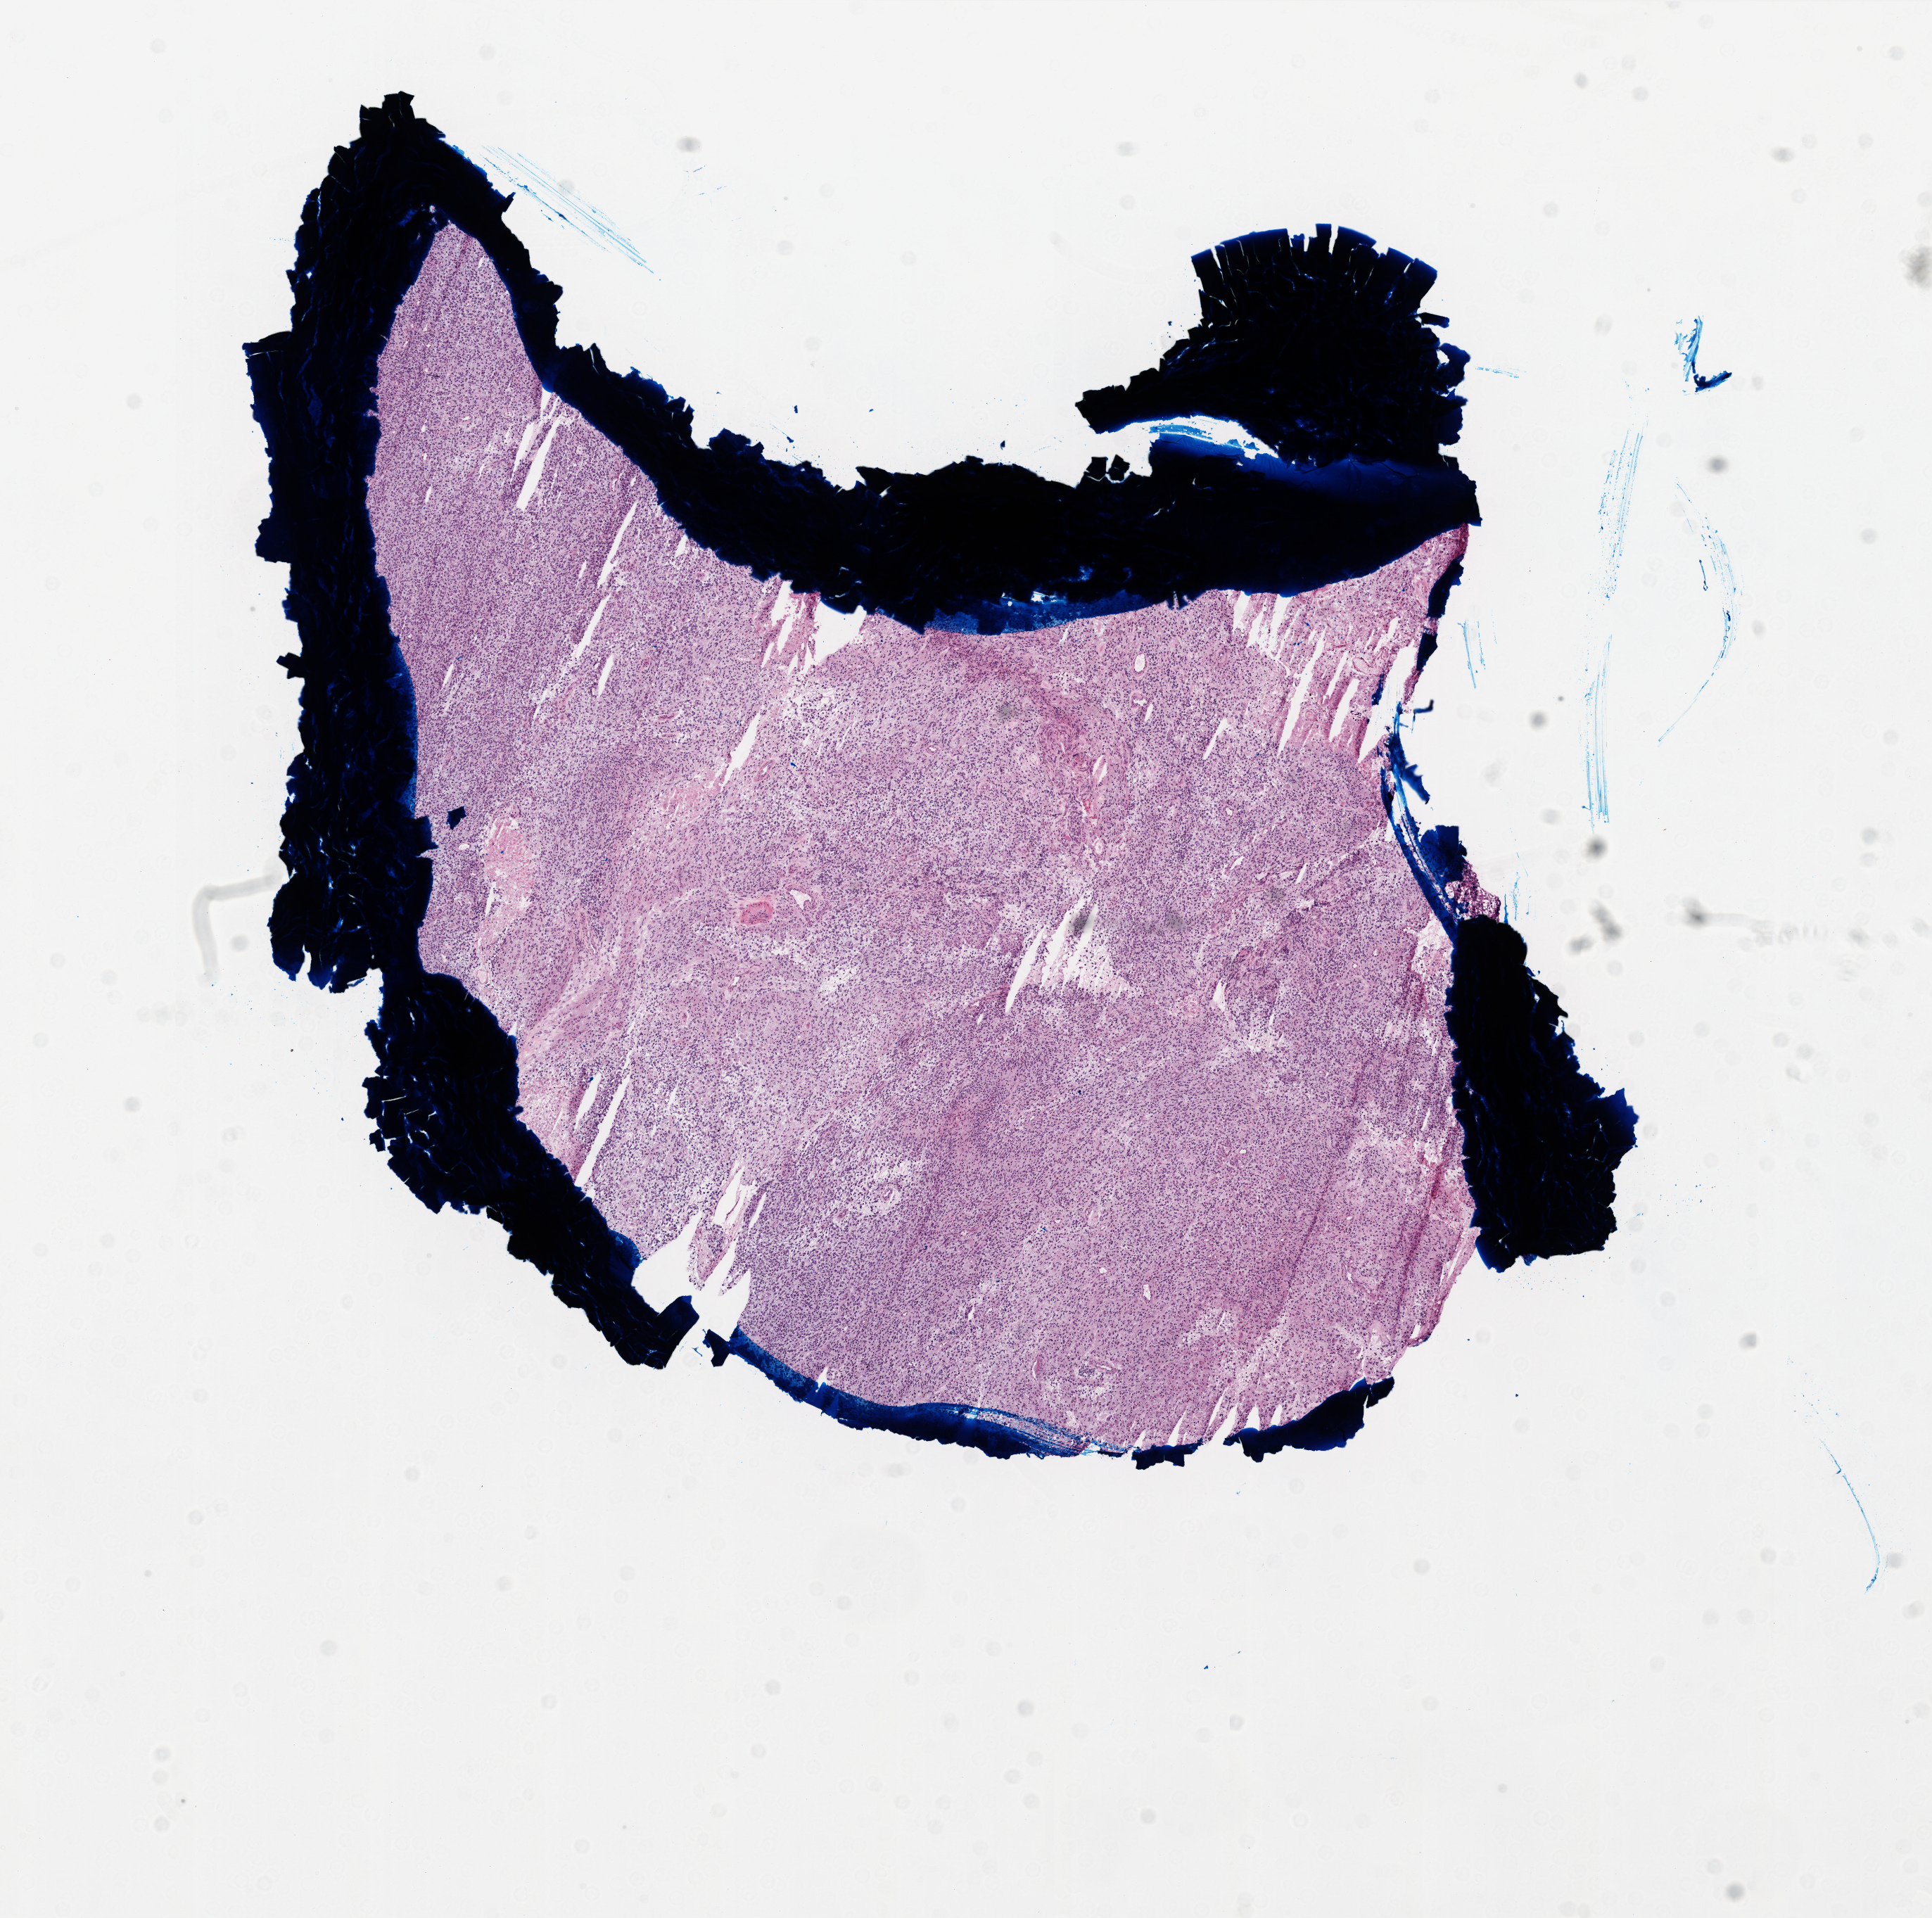
H&E-stained whole-slide image, a low-resolution overview of the entire scanned area, about 11.0 x 10.9 mm. Frozen section from the top of the tissue portion. Sample: primary tumour, brain. Patient: male, age at initial diagnosis 76 years.
Histologic diagnosis: Glioblastoma.